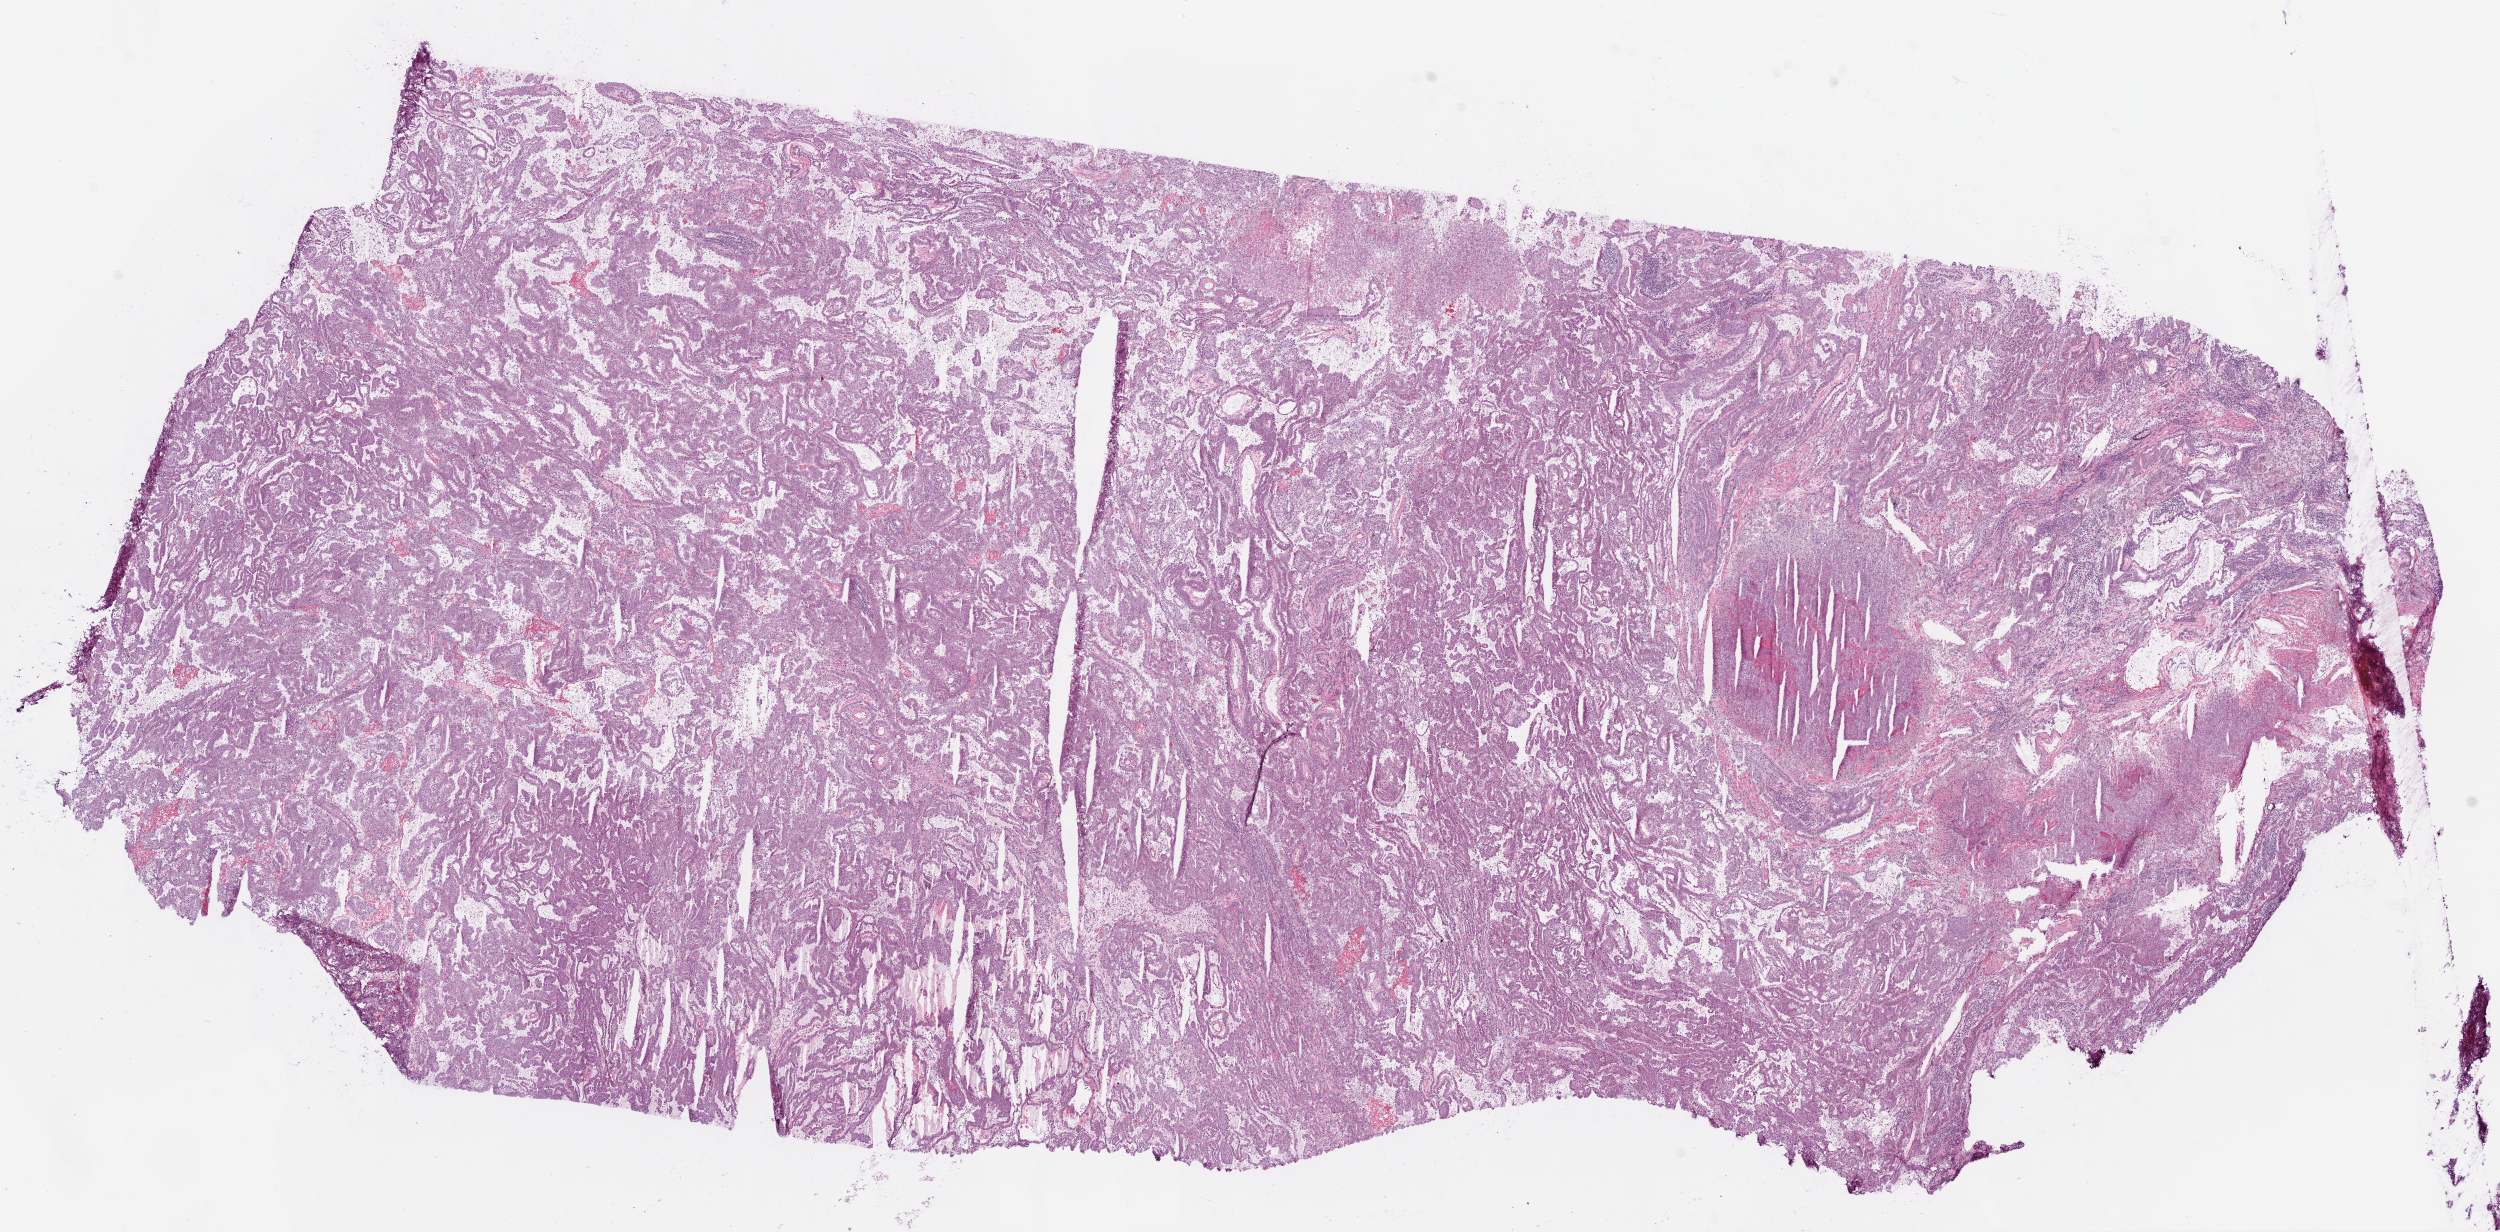
Whole-slide histology image, Hematoxylin and eosin (H&E) stained — low-resolution overview of the scanned area, about 20.1 x 9.9 mm; frozen section; kidney, primary tumour sample. Patient: female, age at initial diagnosis 72 years. Histologic grade: G2 (moderately differentiated). Composition of this section per pathologist review: tumour cells 97%, tumour nuclei 93%, normal cells 0%, stromal cells 0%, necrosis 3%. Inflammatory infiltration, as recorded: lymphocyte infiltration 3%, monocyte infiltration 0%, neutrophil infiltration 0%.
Laterality: left. Diagnosis: Clear cell adenocarcinoma, NOS. AJCC pathologic stage: I. TNM: T1b NX M0.